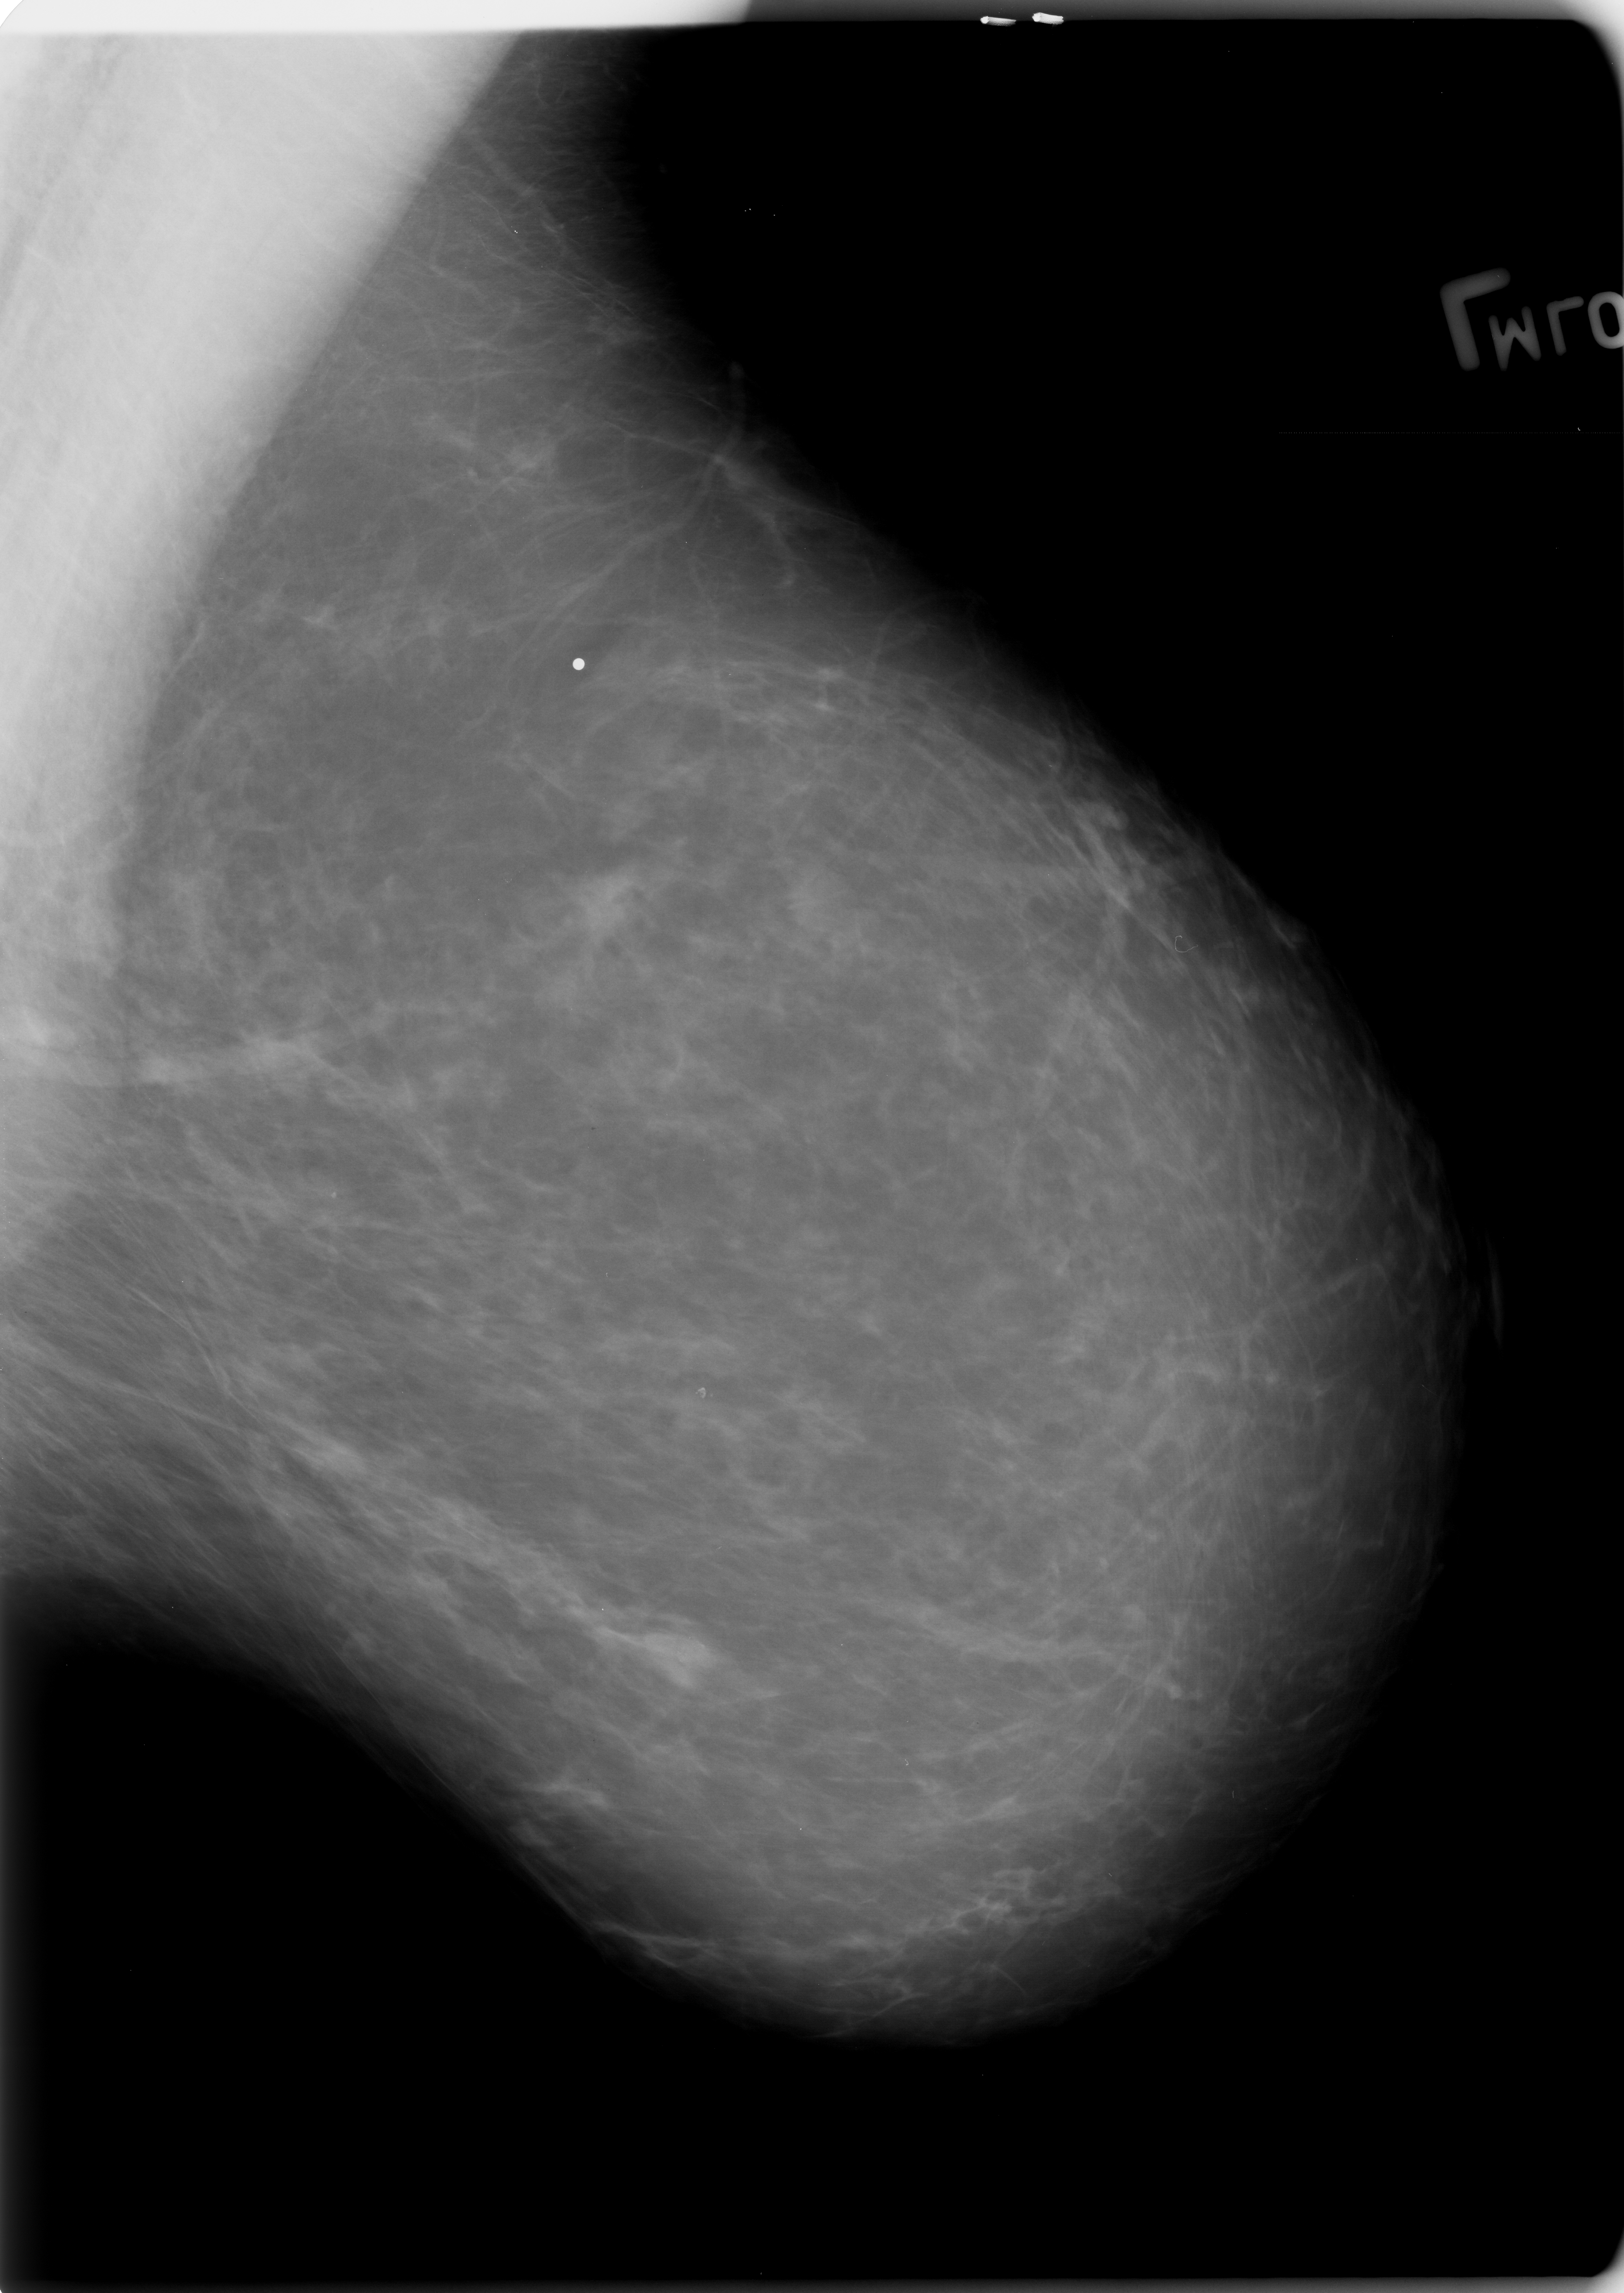
Mammogram (digitized film), left breast, mediolateral oblique (MLO) view, breast composition: scattered fibroglandular densities (BI-RADS density category 2 of 4).
Finding: calcifications, morphology amorphous, distribution clustered; BI-RADS assessment category 4; pathology result (as recorded, not read from the image): benign.